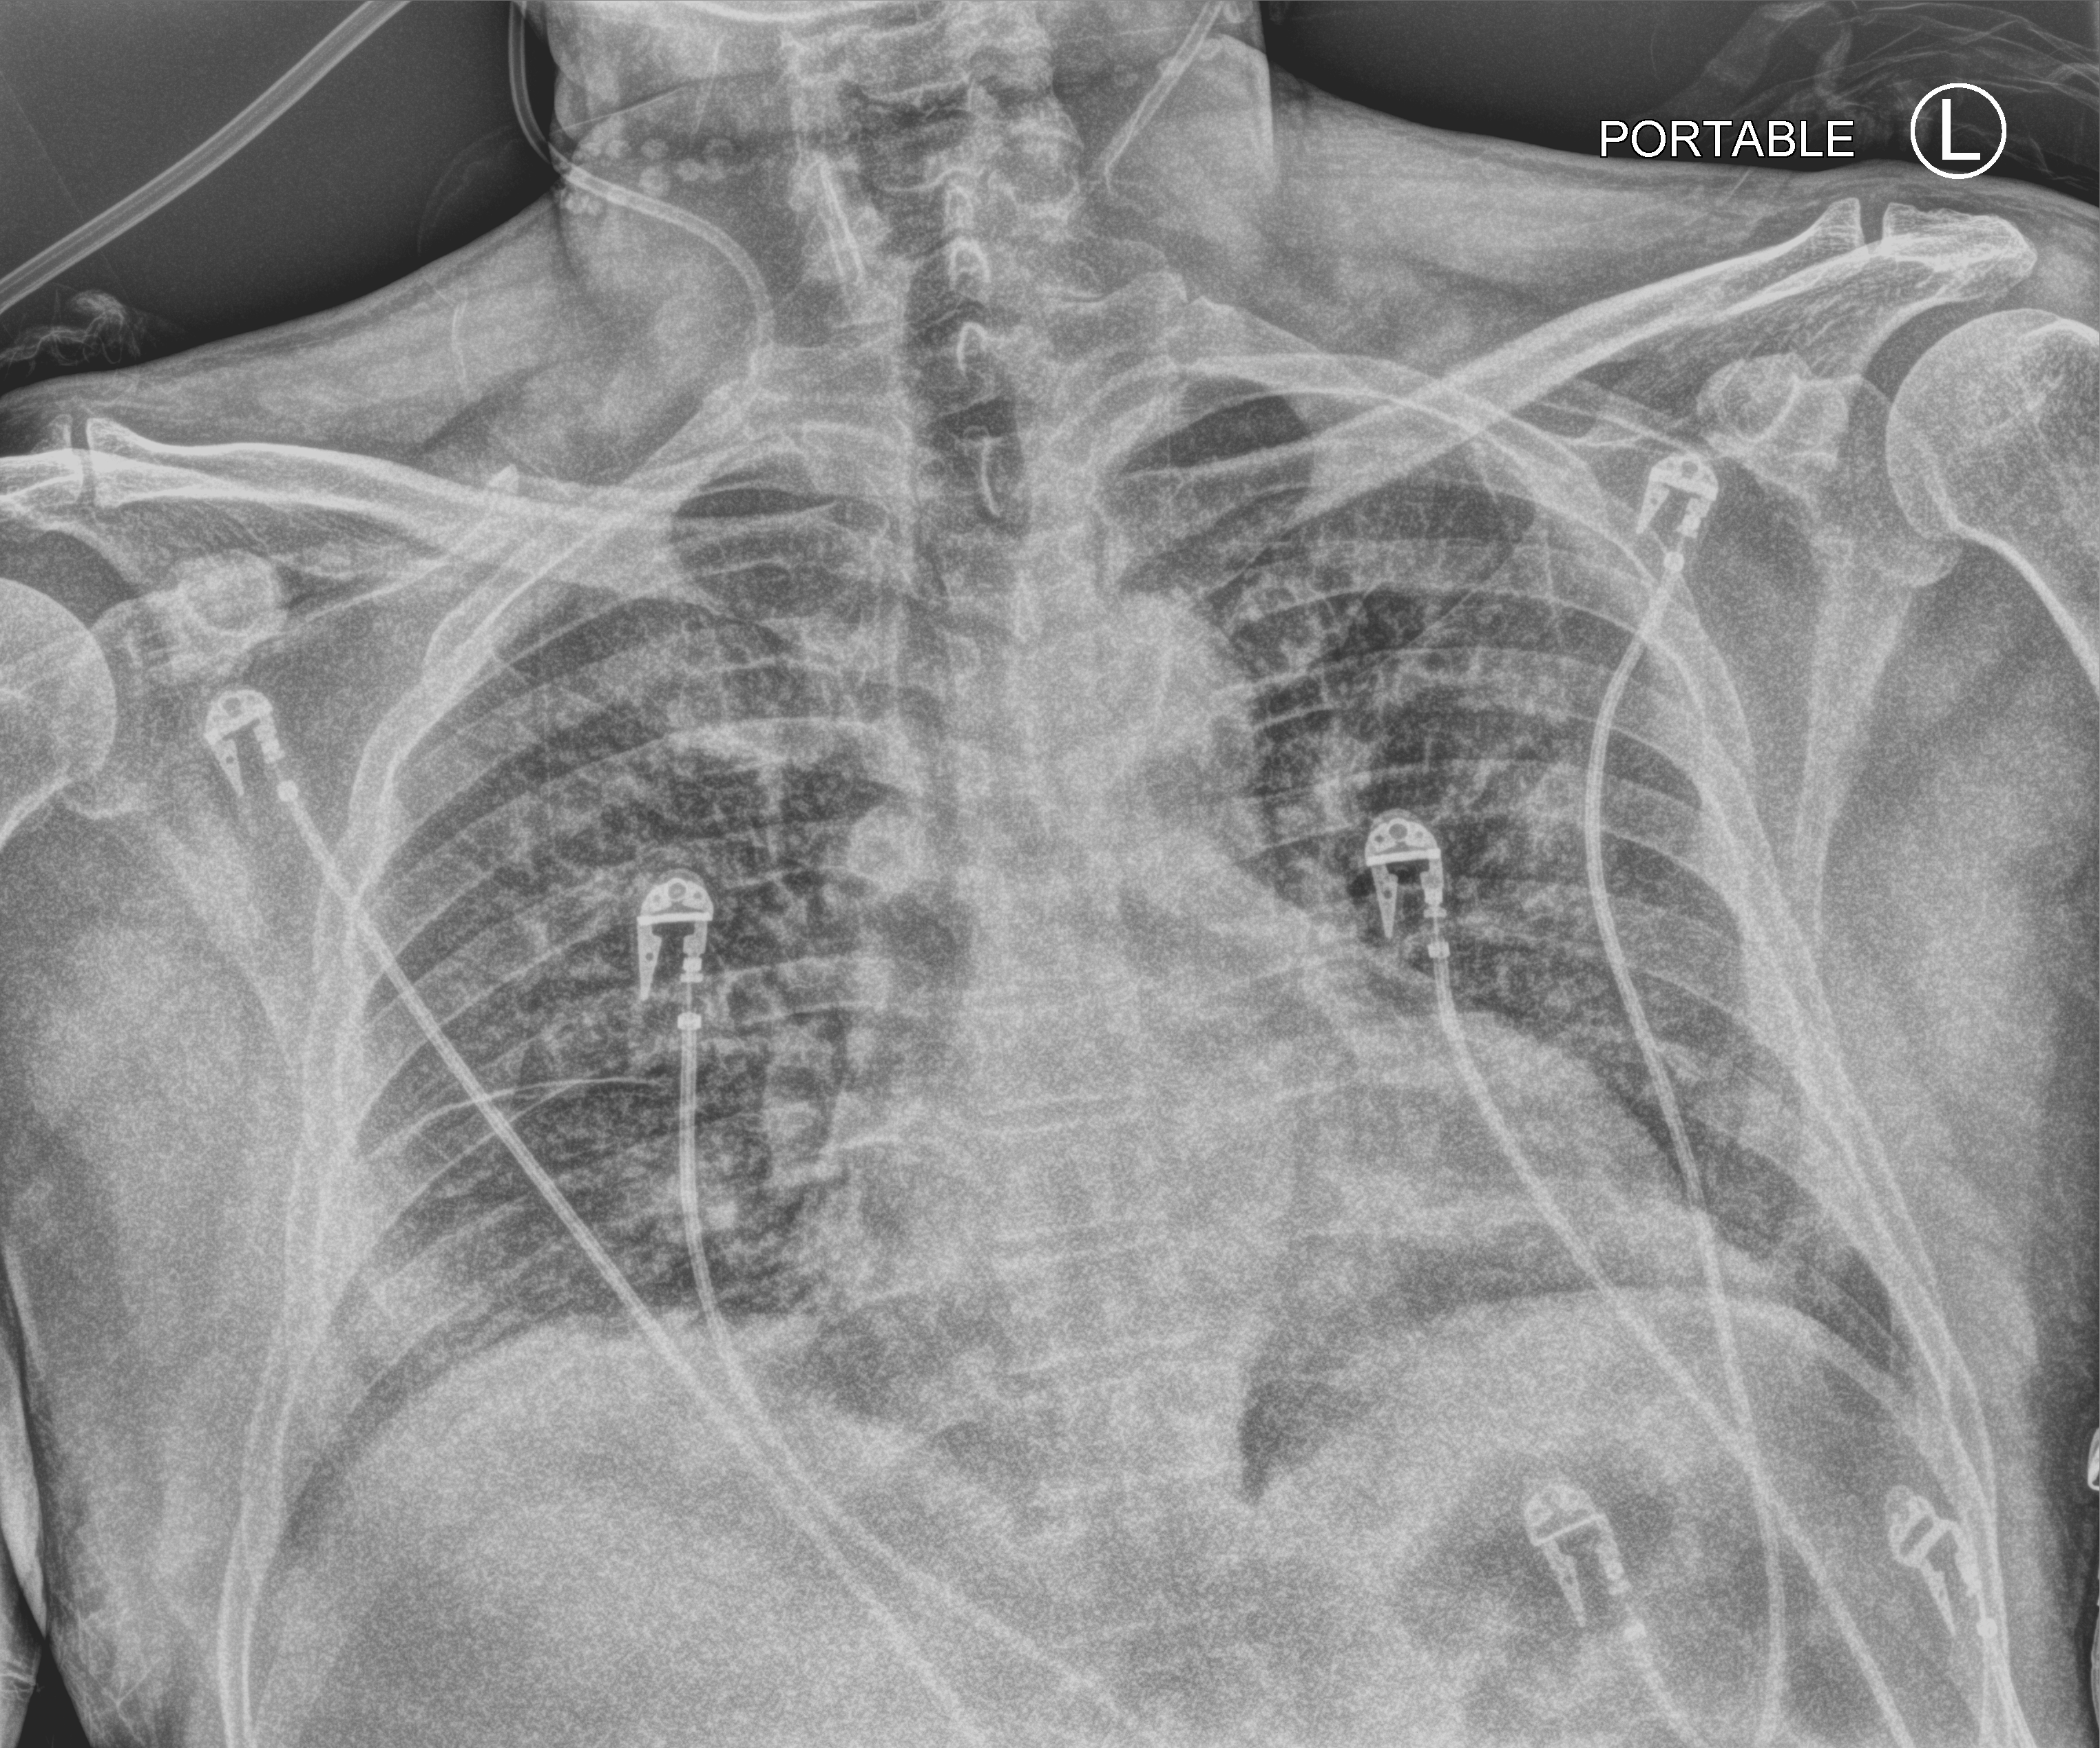
Bedside chest radiograph (computed radiography). Patient hospitalised with COVID-19; male, aged 18–59 years.
From the hospital-stay record, not from the radiograph (when in the stay this image was taken is not recorded):
- COPD (admission record): no